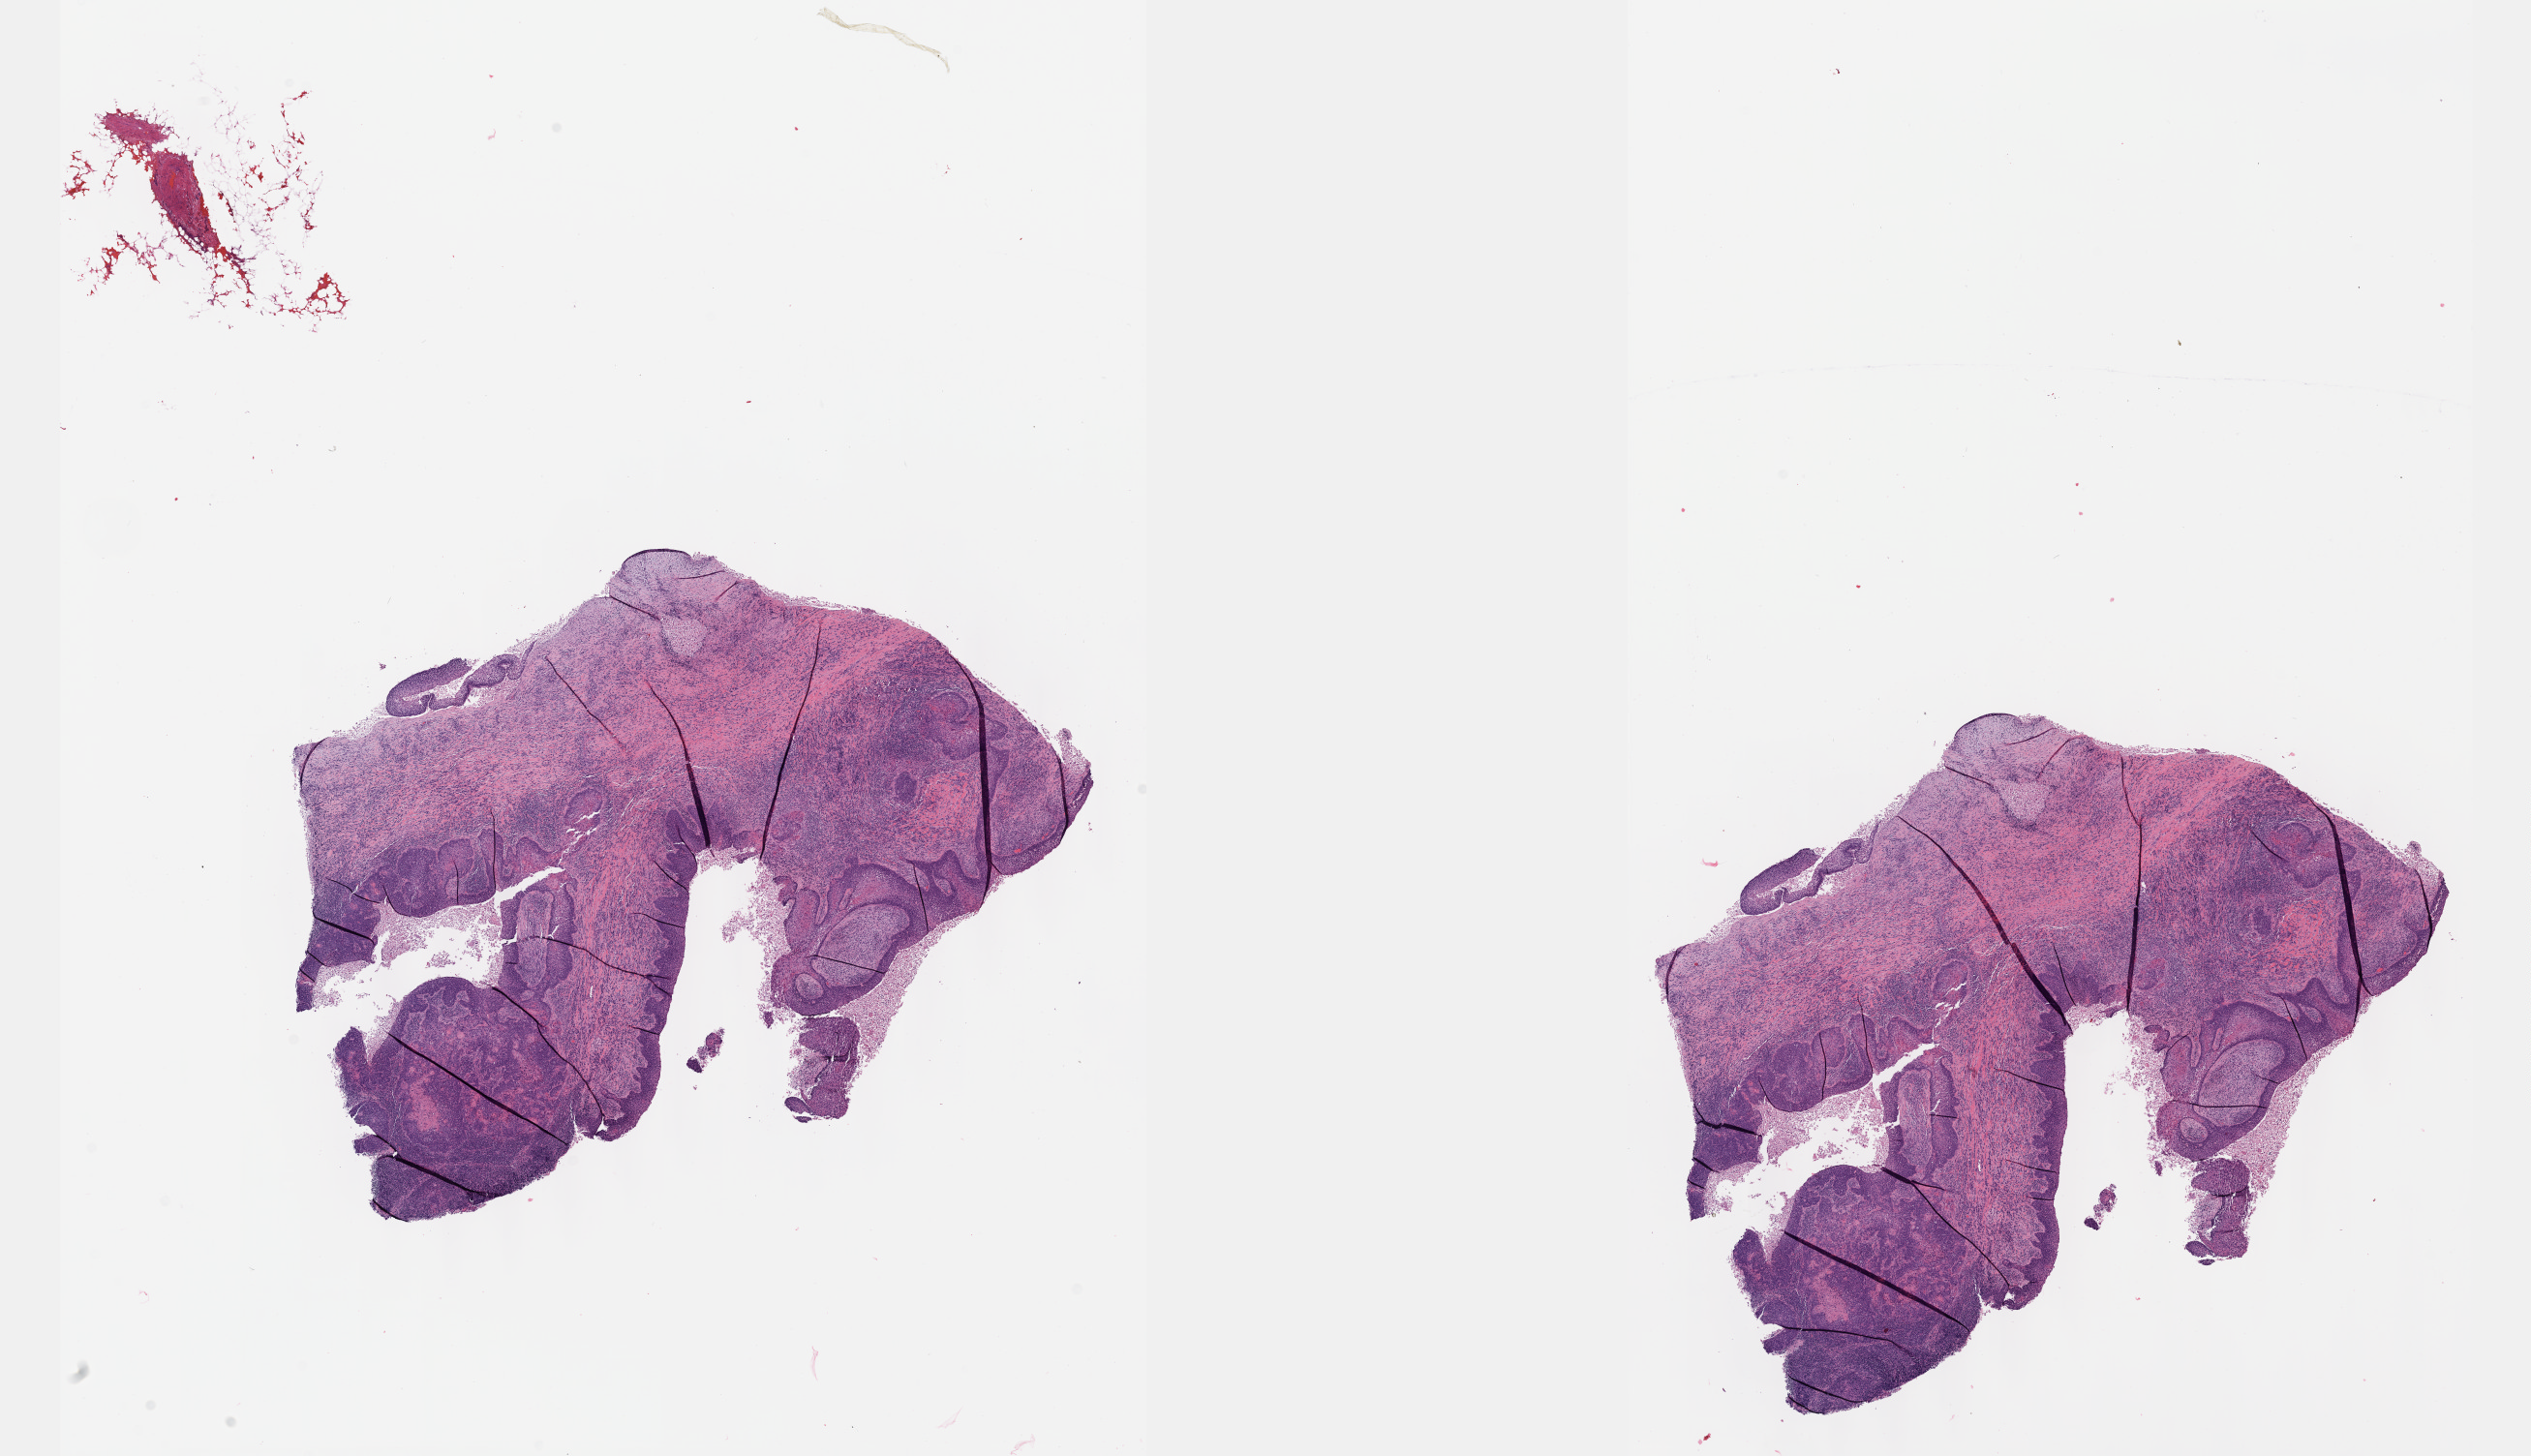
Digitized H&E tissue section (whole slide) — a low-resolution overview of the entire scanned area, about 21.1 x 12.2 mm, FFPE section, primary tumour sample from the head and neck. Patient: male, age at initial diagnosis 57 years. Histologic grade: G2 (moderately differentiated).
* histologic diagnosis: Squamous cell carcinoma, keratinizing, NOS (tonsil, NOS)
* laterality: right